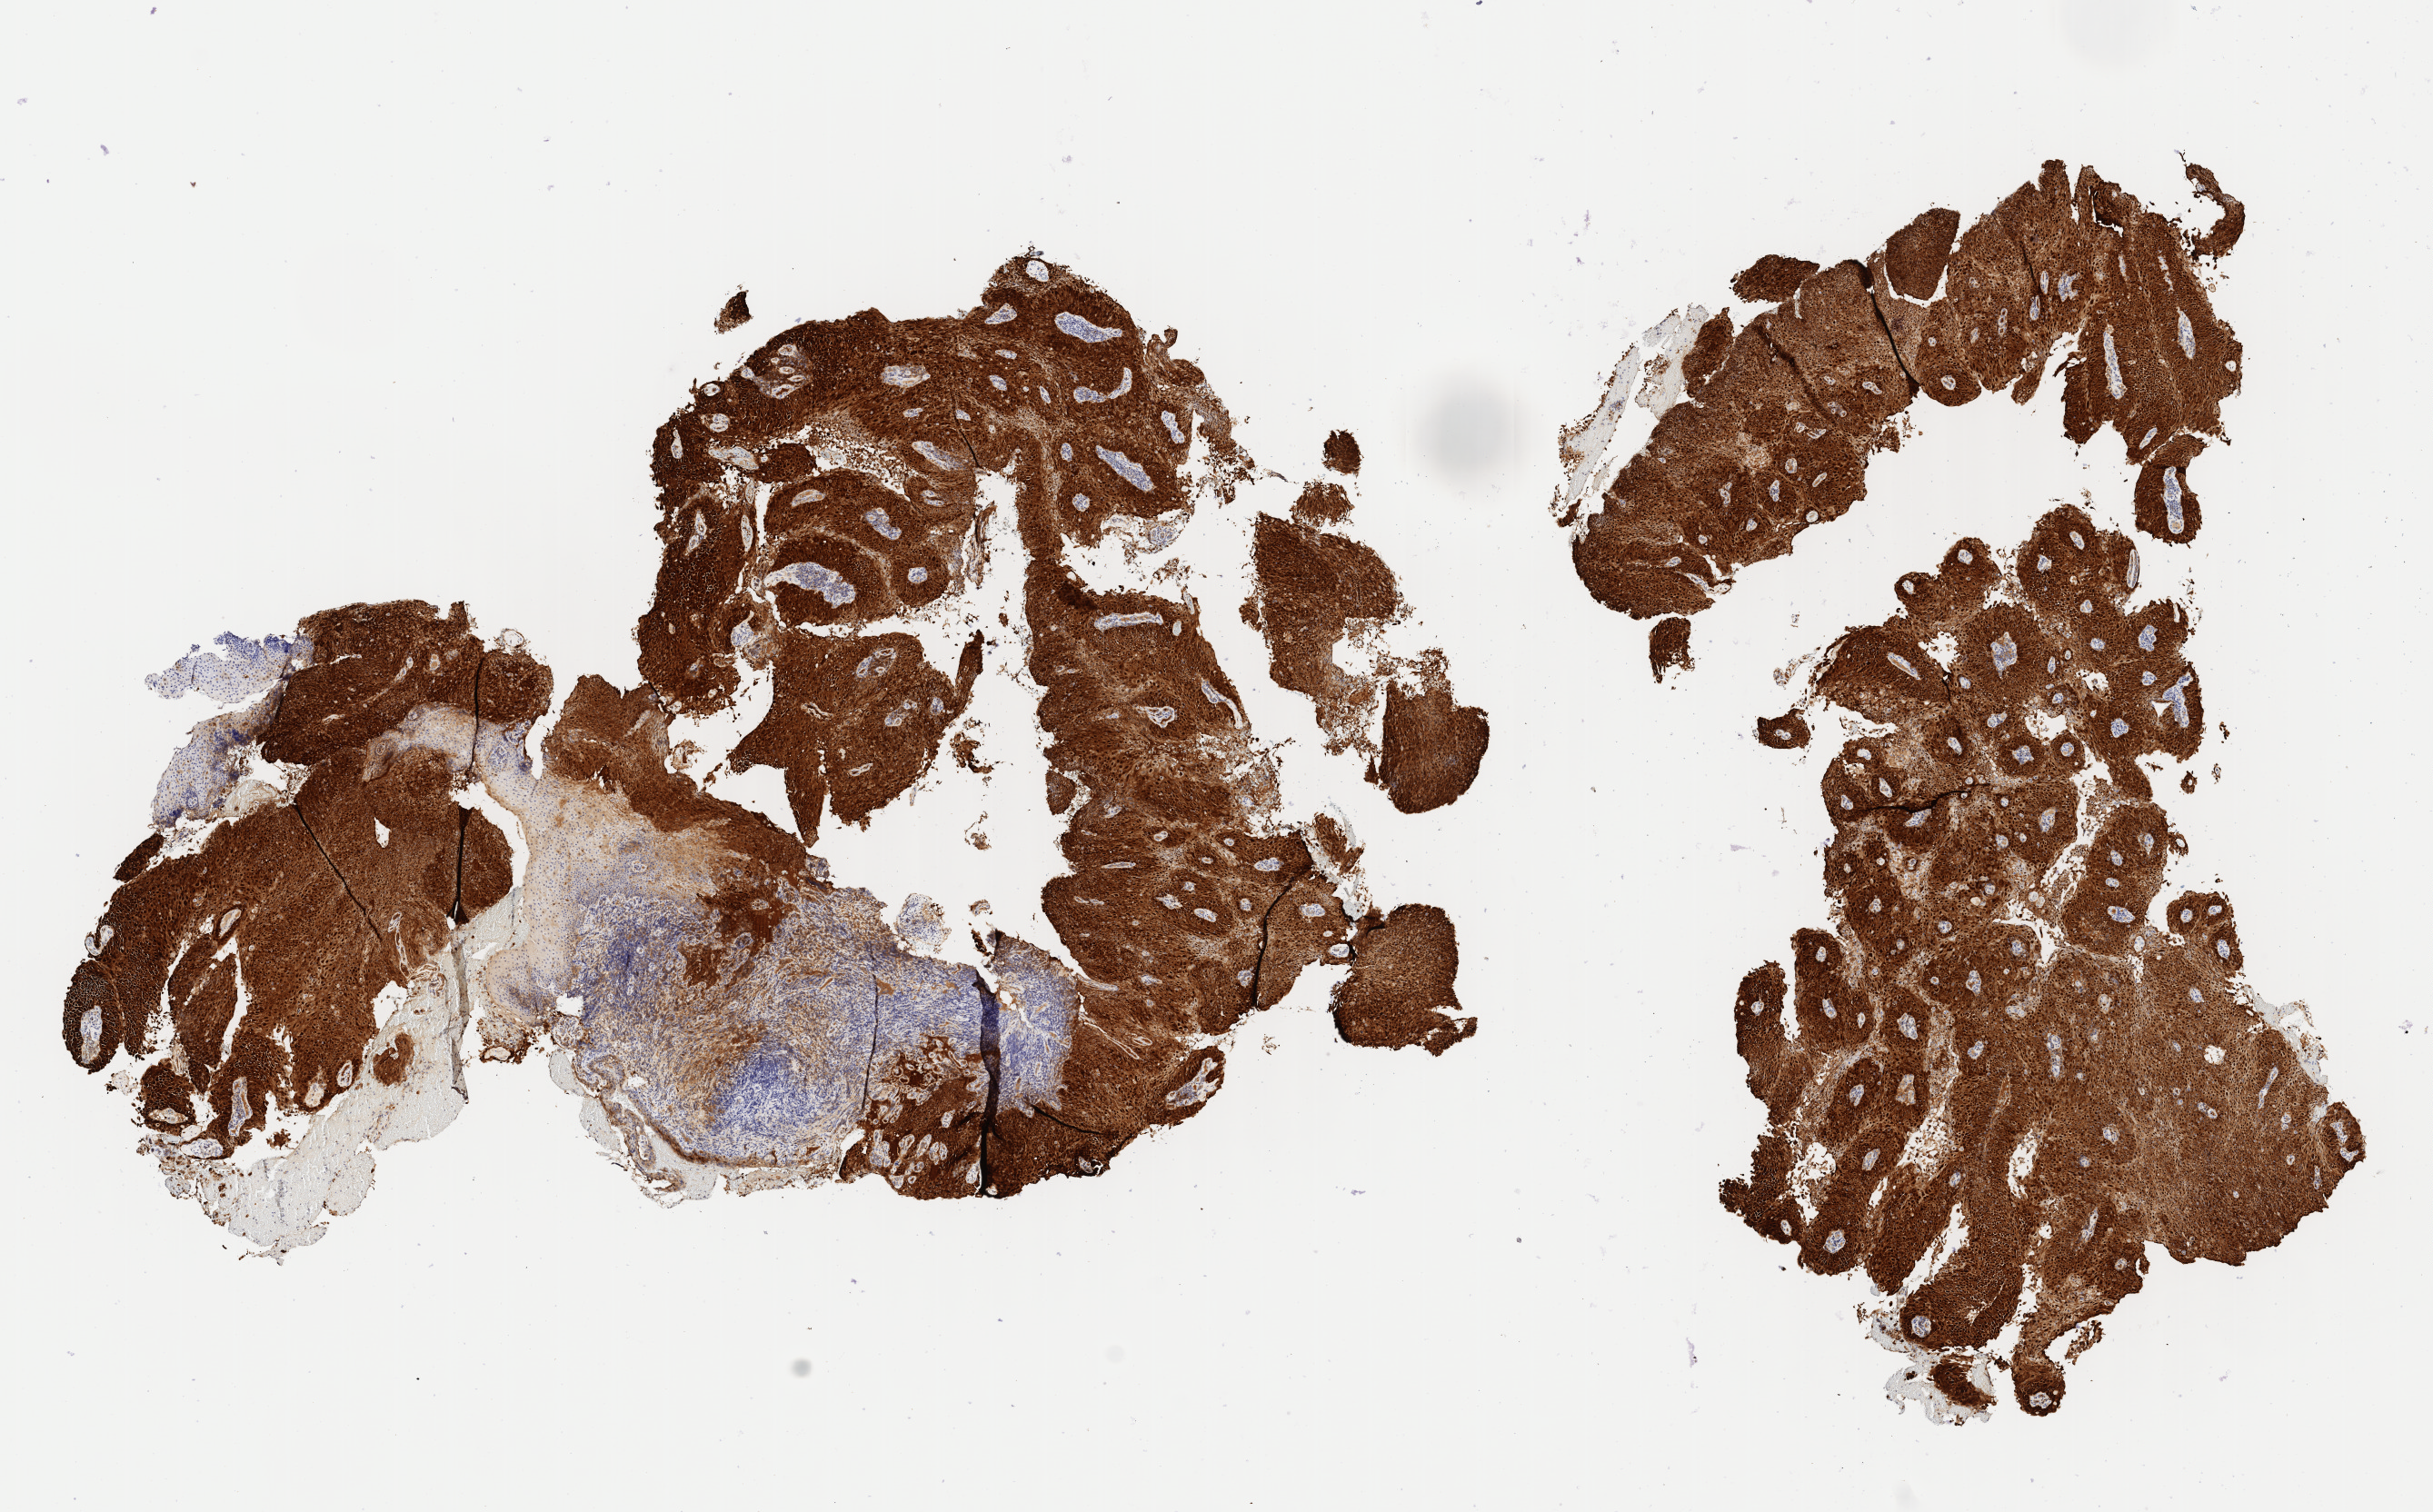
Whole-slide image, immunohistochemical stain for p16 (p16INK4a) — whole scanned area (about 10.7 x 6.6 mm) shown as a low-resolution overview, tumor tissue, site: cervix. Patient female; 82 years old.
Histologic diagnosis: Squamous cell carcinoma, keratinizing, NOS.